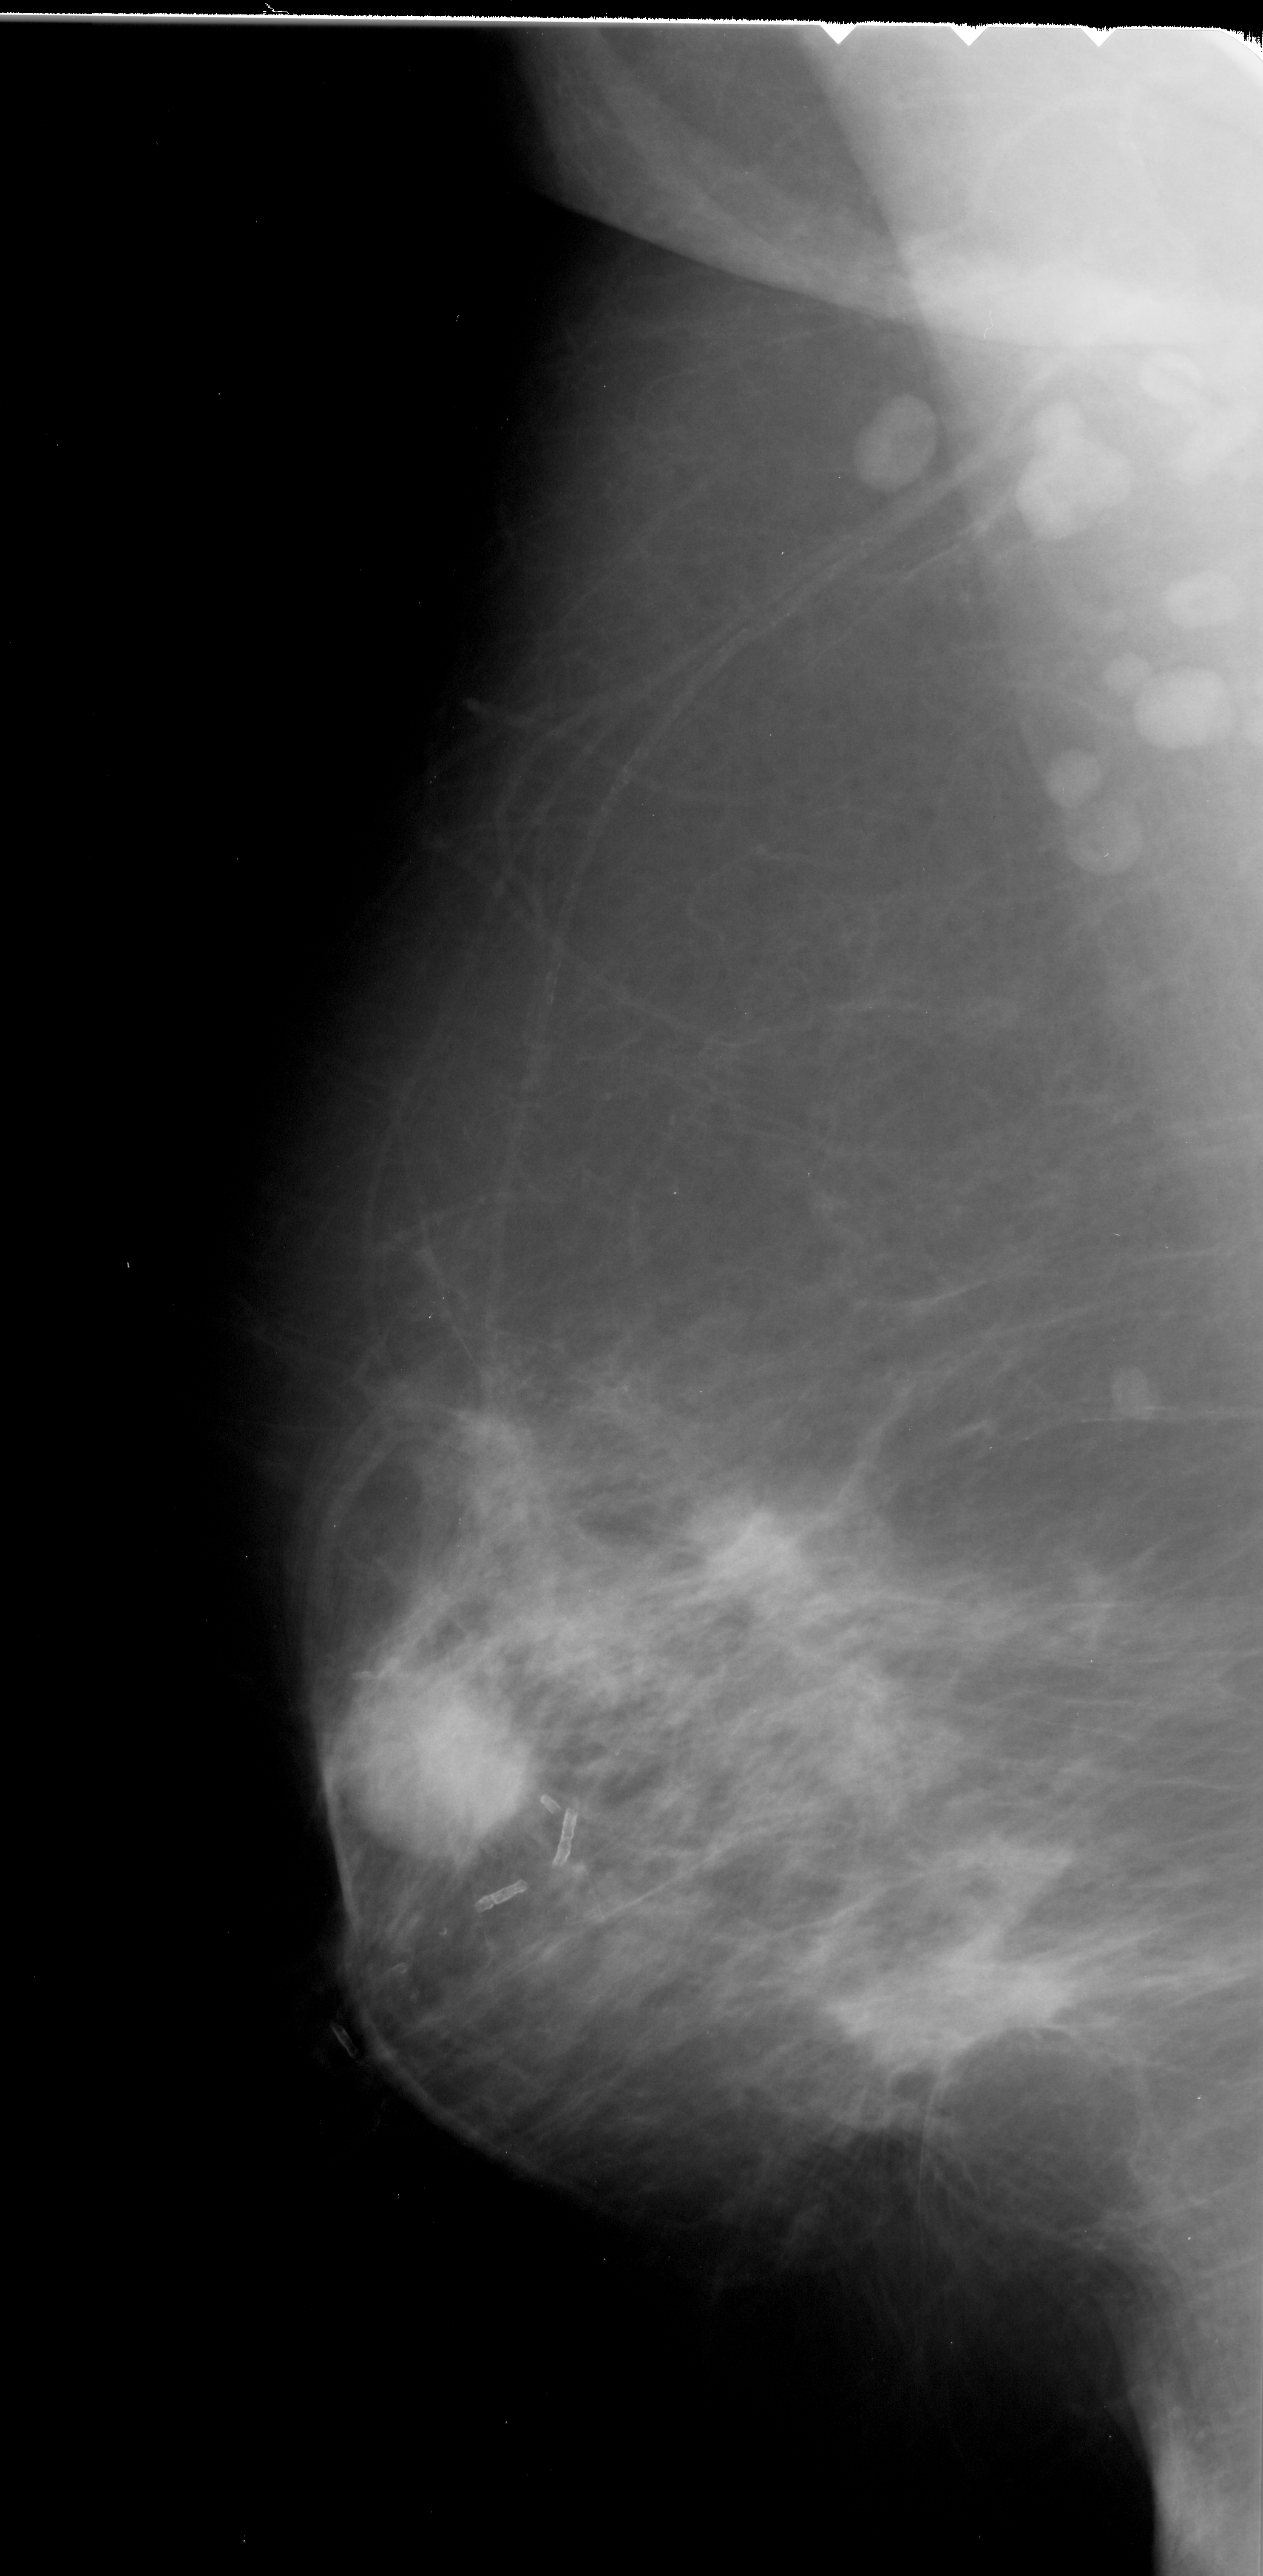
Digitized screen-film mammogram; left breast; mediolateral oblique (MLO) view; breast composition: scattered fibroglandular densities (BI-RADS density category 2 of 4); 1263 × 2576 image matrix.
Expert-marked regions of interest on this image (one box per marked abnormality):
- Finding 1 of 2: mass, shape round, margins spiculated; BI-RADS assessment category 5; subtlety rating 5 on a 1 (subtle) to 5 (obvious) scale; pathology result (as recorded, not read from the image): malignant: box from (x=393, y=1652) to (x=551, y=1823) px
- Finding 2 of 2: mass, shape irregular, margins spiculated; BI-RADS assessment category 5; pathology (as recorded): malignant: (x=883, y=1919)–(x=1062, y=2102)